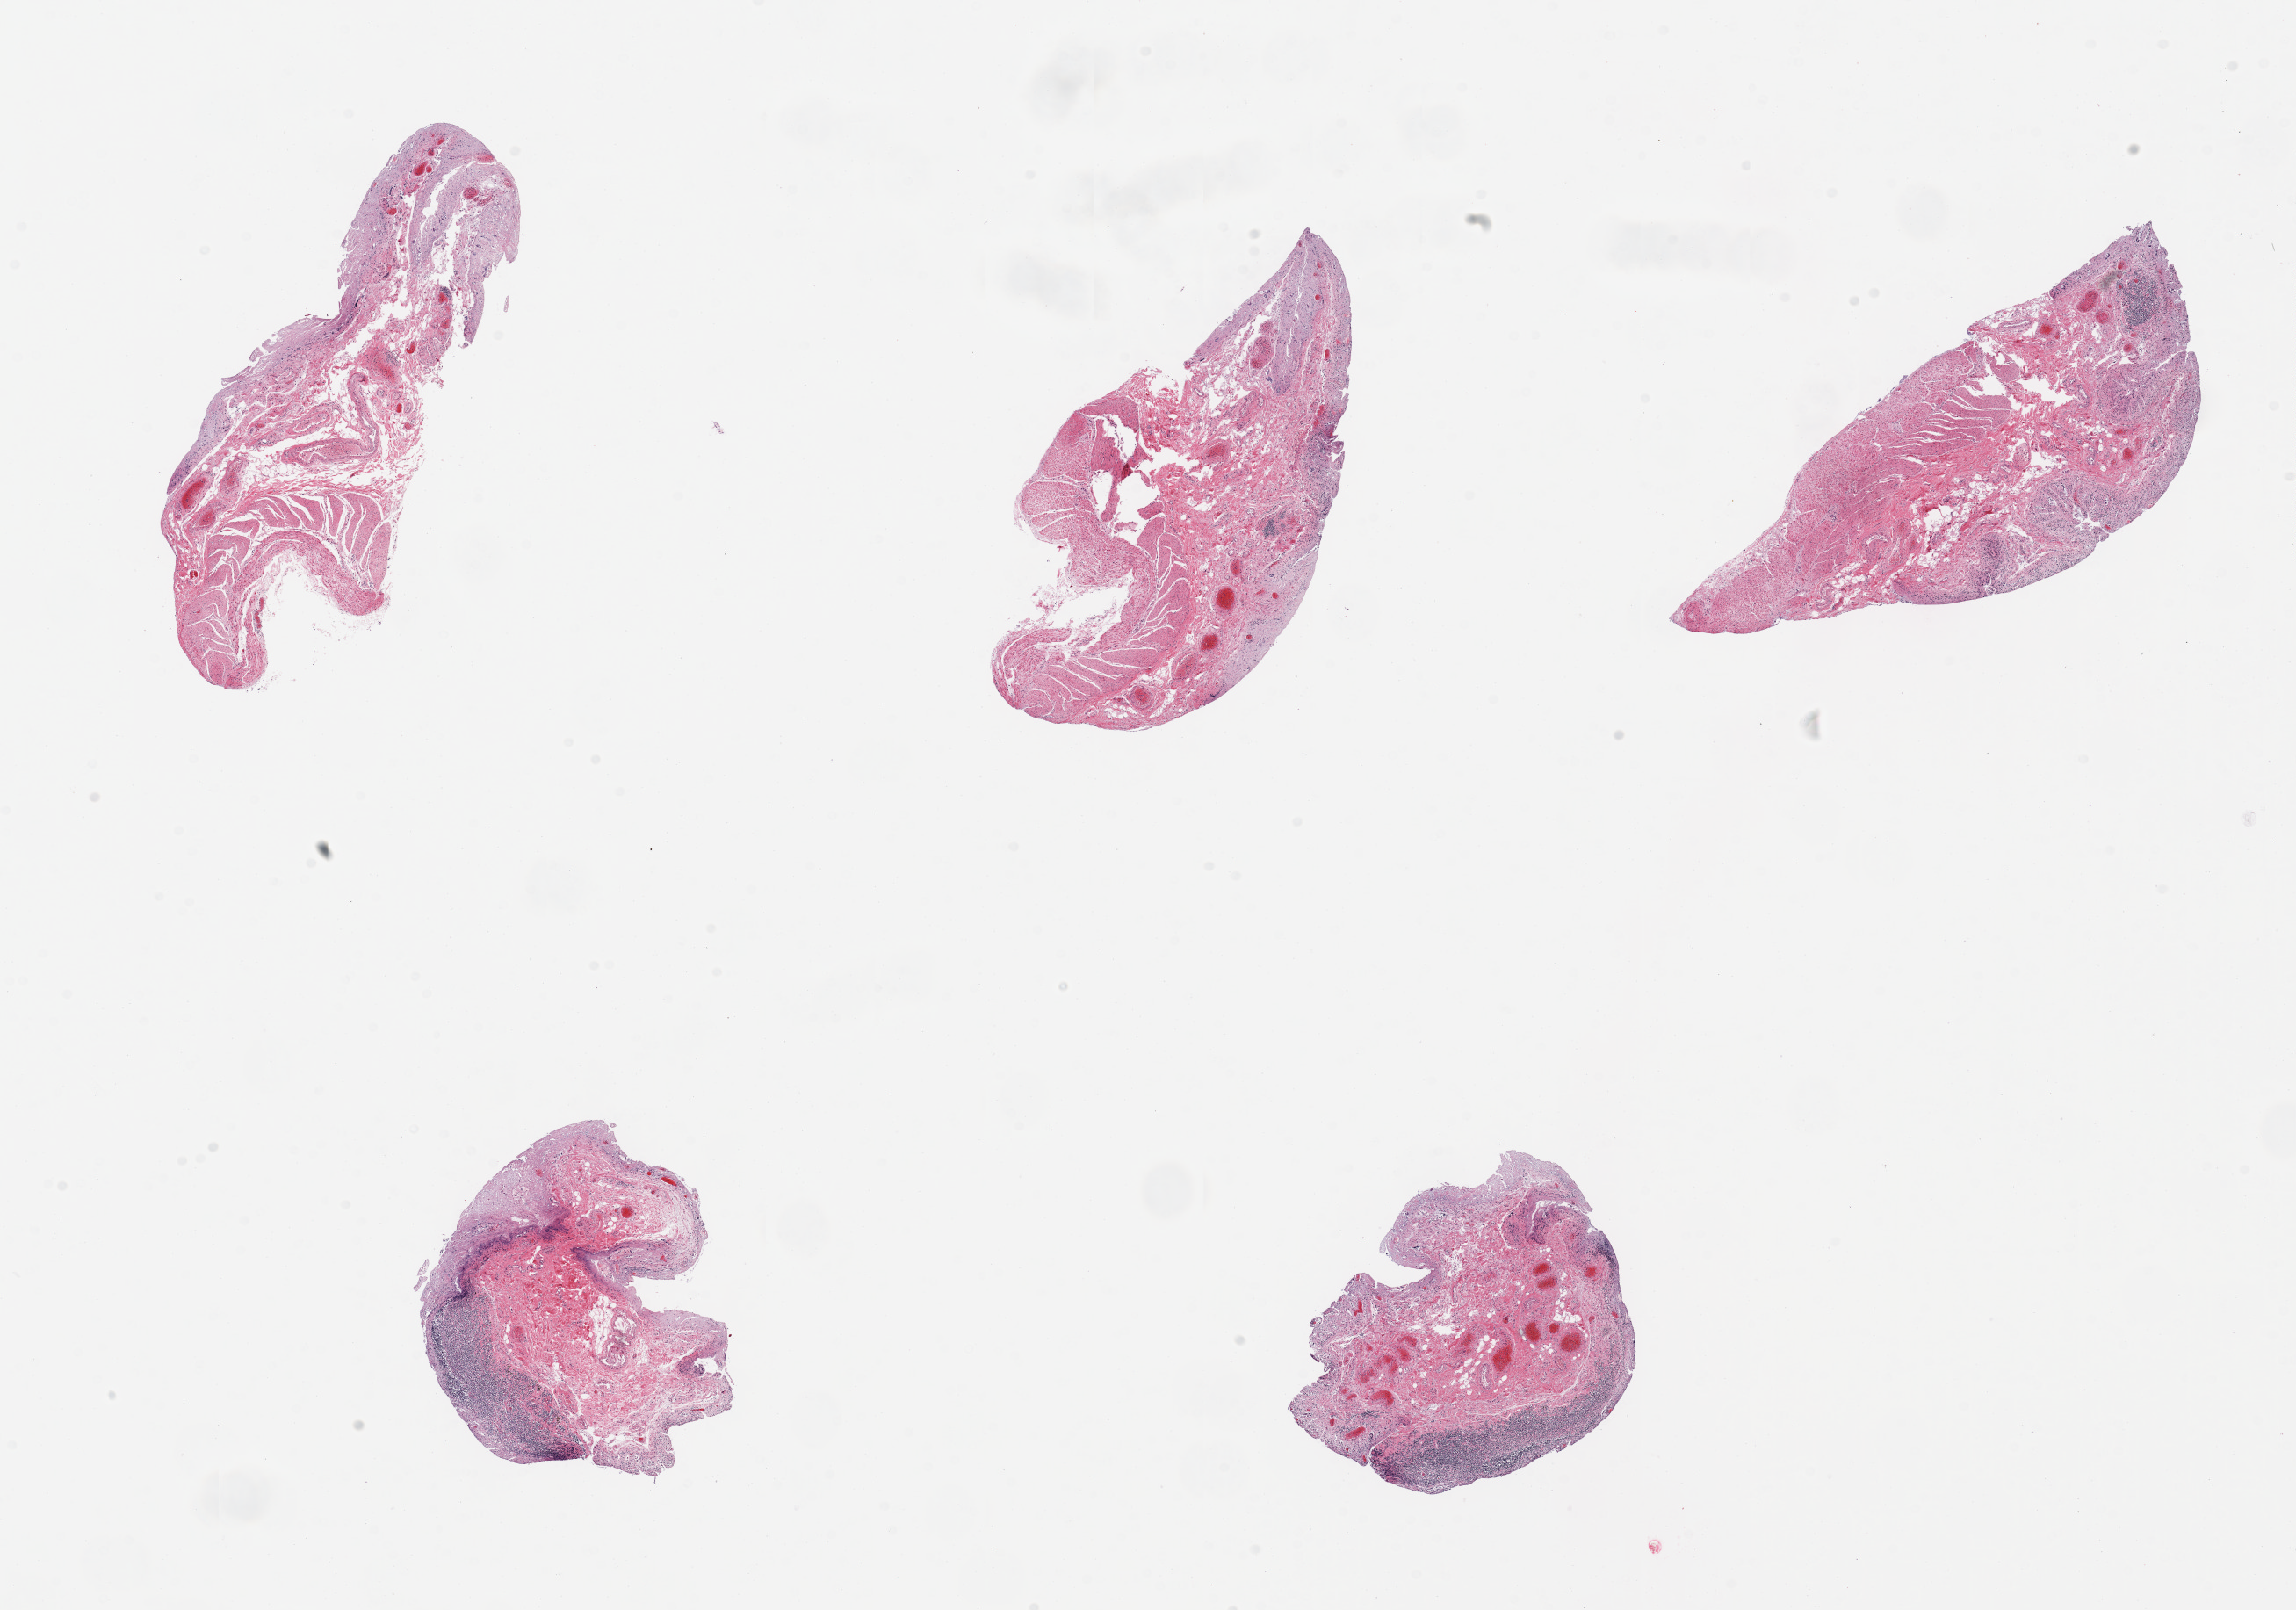
Whole-slide image, haematoxylin and eosin stain, brightfield, shown as a low-resolution overview of the whole scanned area (about 20.7 x 14.5 mm, slide scanned at 20x); PAXgene-fixed paraffin-embedded (PFPE) section; sampled site (target tissue): ileum; donor tissue sample. Donor sex: female.
Review note (as recorded): 5 pieces, ~10-20 lymphoid aggregates.